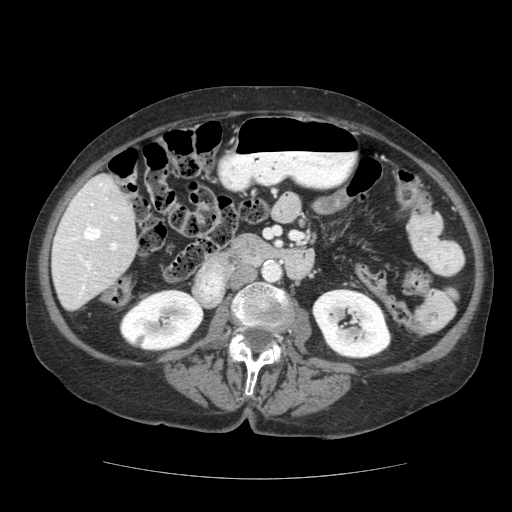
Contrast-enhanced abdominal CT (liver protocol), one axial slice. Position 49 of 111 along the scan axis. Reconstruction kernel STANDARD. Soft-tissue window (W 400 / L 40 HU). 2.5 mm slice thickness. 512 × 512 image matrix, field of view 360 × 360 mm. From the clinical record (not read from this slice): diagnosis: hepatocellular carcinoma (patient treated with transarterial chemoembolisation; whether this scan precedes or follows treatment is not stated here); TNM stage (as recorded): Stage-I; Child-Pugh class: A; tumour nodularity: uninodular; tumour size: 7.3 cm.
Structures marked on this image (semi-automatically segmented with operator editing):
- liver parenchyma outside the tumour (the mass and vessels are separate outlines, so this box may not span the whole liver): box from (x=52, y=174) to (x=138, y=310) px
- liver vessels: (x=56, y=183)–(x=118, y=299)